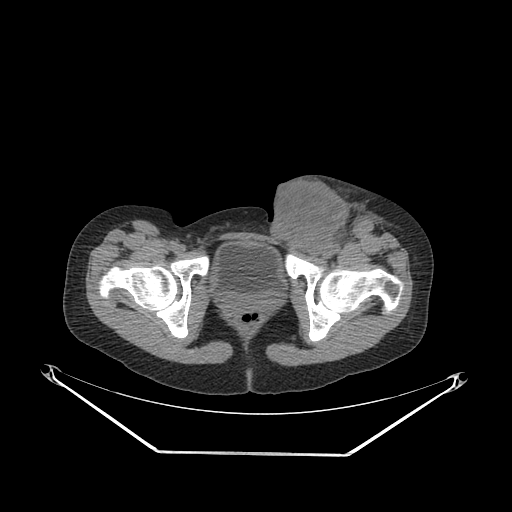
CT of an extremity soft-tissue mass (from a PET/CT study), one axial slice. Position 67 of 267 along the scan axis. Soft-tissue window (W 400 / L 40 HU). 3.75 mm slice thickness. 512 × 512 image matrix, field of view 500 × 500 mm. Female patient. Case-level facts recorded for this patient, not image findings: histological type: leiomyosarcoma; grade: high; site of the primary tumour: groin.
Outlined on this slice (expert contour drawn on MRI and transferred to this co-registered scan by the dataset authors):
- gross tumour volume including surrounding oedema: bounding box (x1, y1, x2, y2) in pixels: (265, 180, 382, 257)
- gross tumour volume (mass): (267, 183, 348, 254)